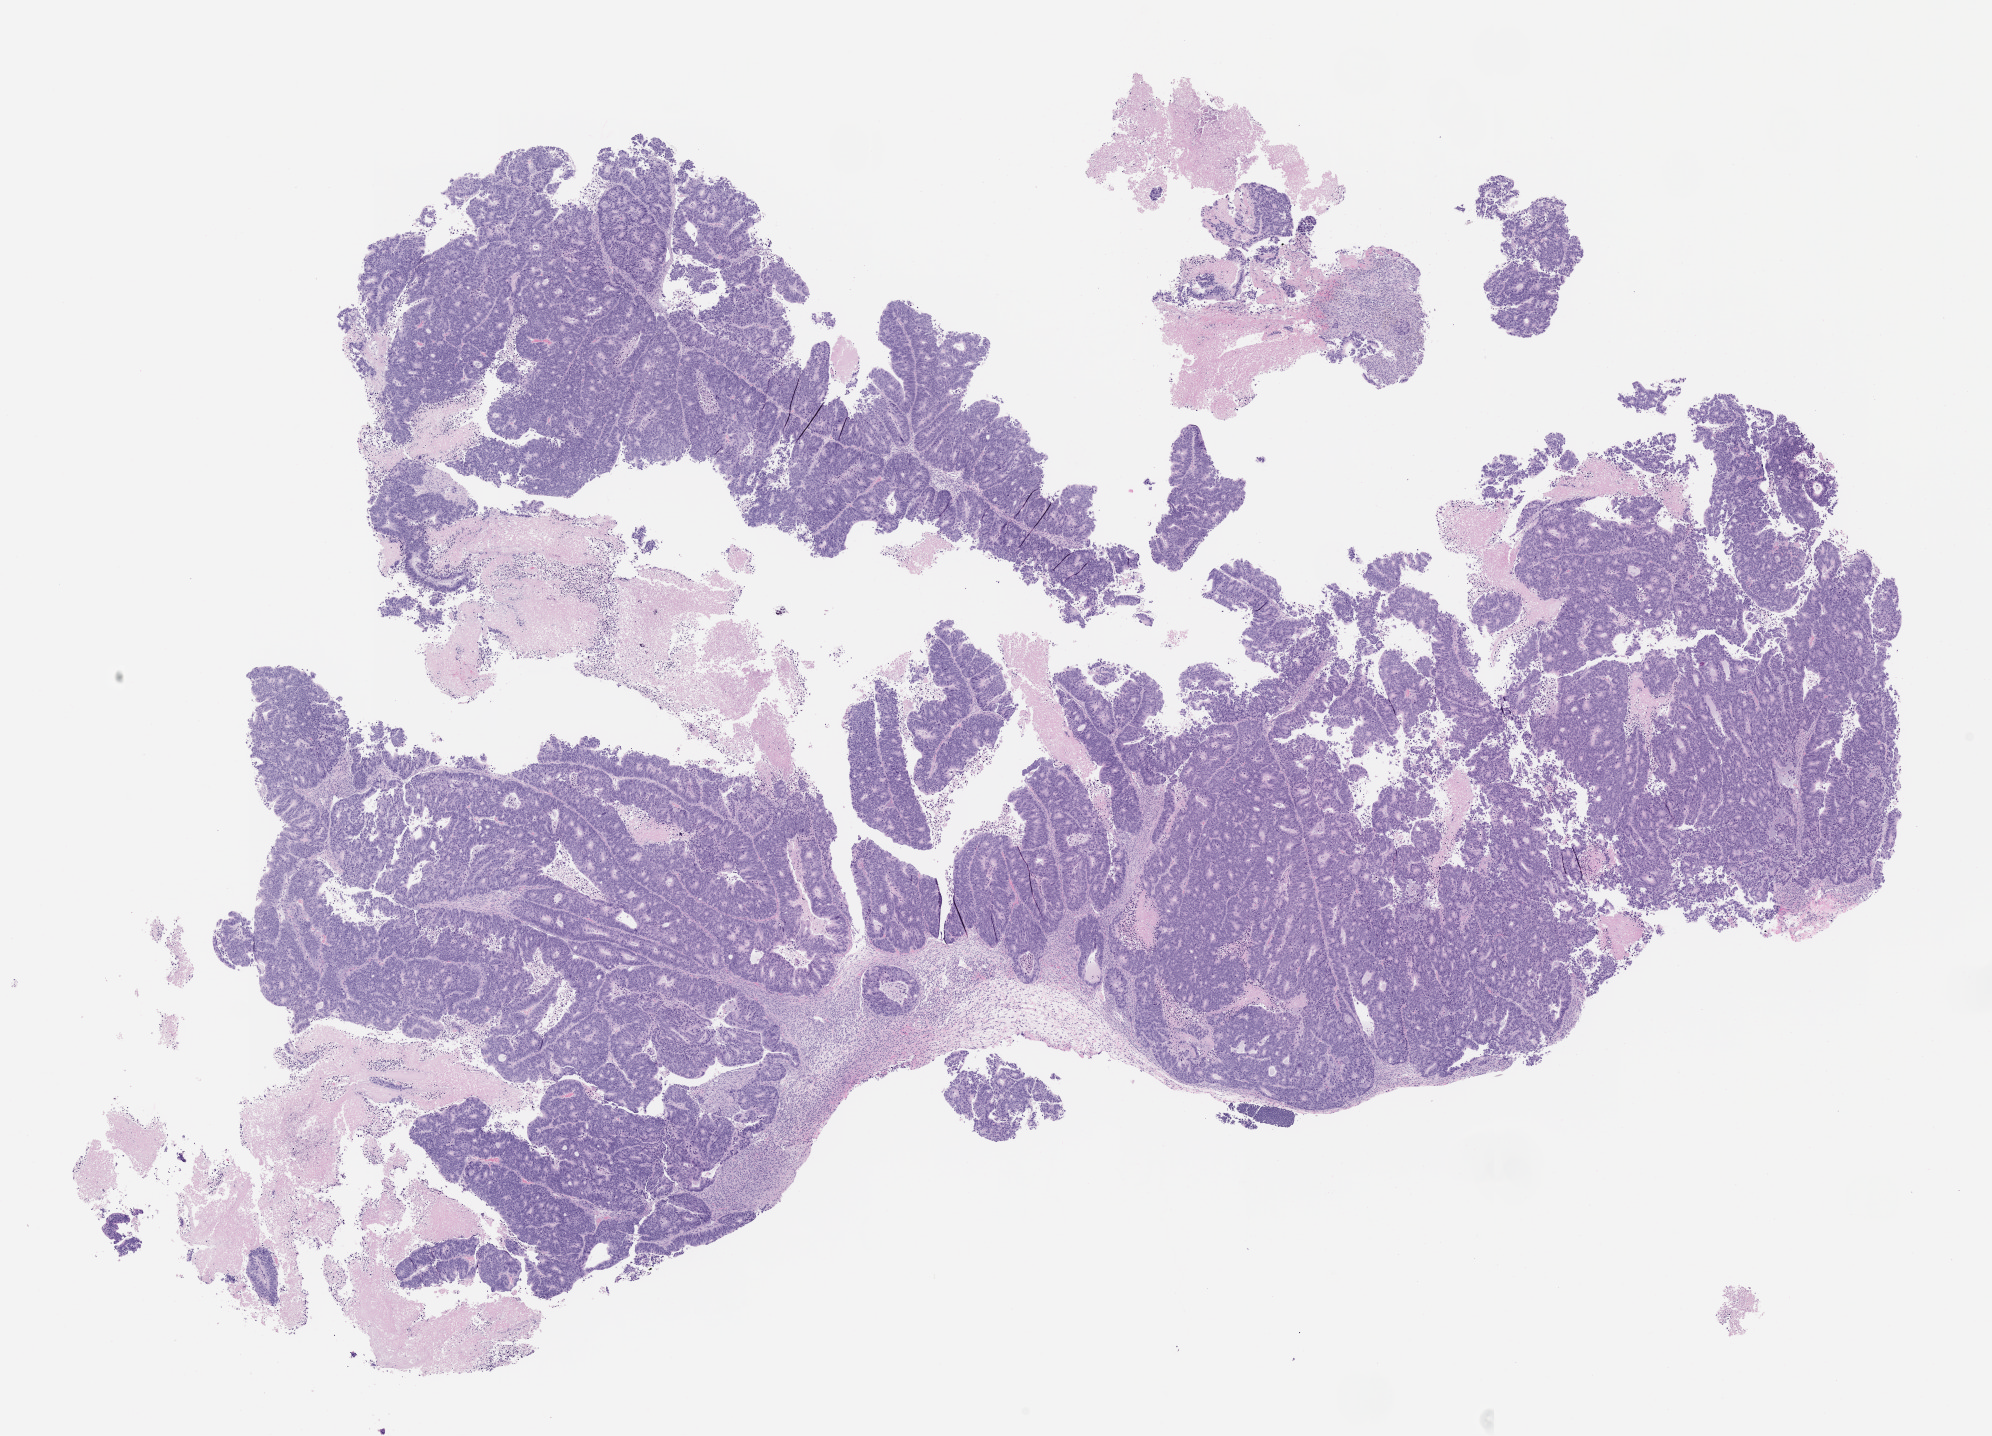
Hematoxylin and eosin (H&E) whole-slide image of a patient-derived xenograft (PDX) tumor grown in a mouse, passage 2 — a low-resolution overview of the entire scanned area, about 16.0 x 11.6 mm. Formalin-fixed paraffin-embedded section. Originating tumor site category: colon.
- originating patient diagnosis: Colon Adenocarcinoma